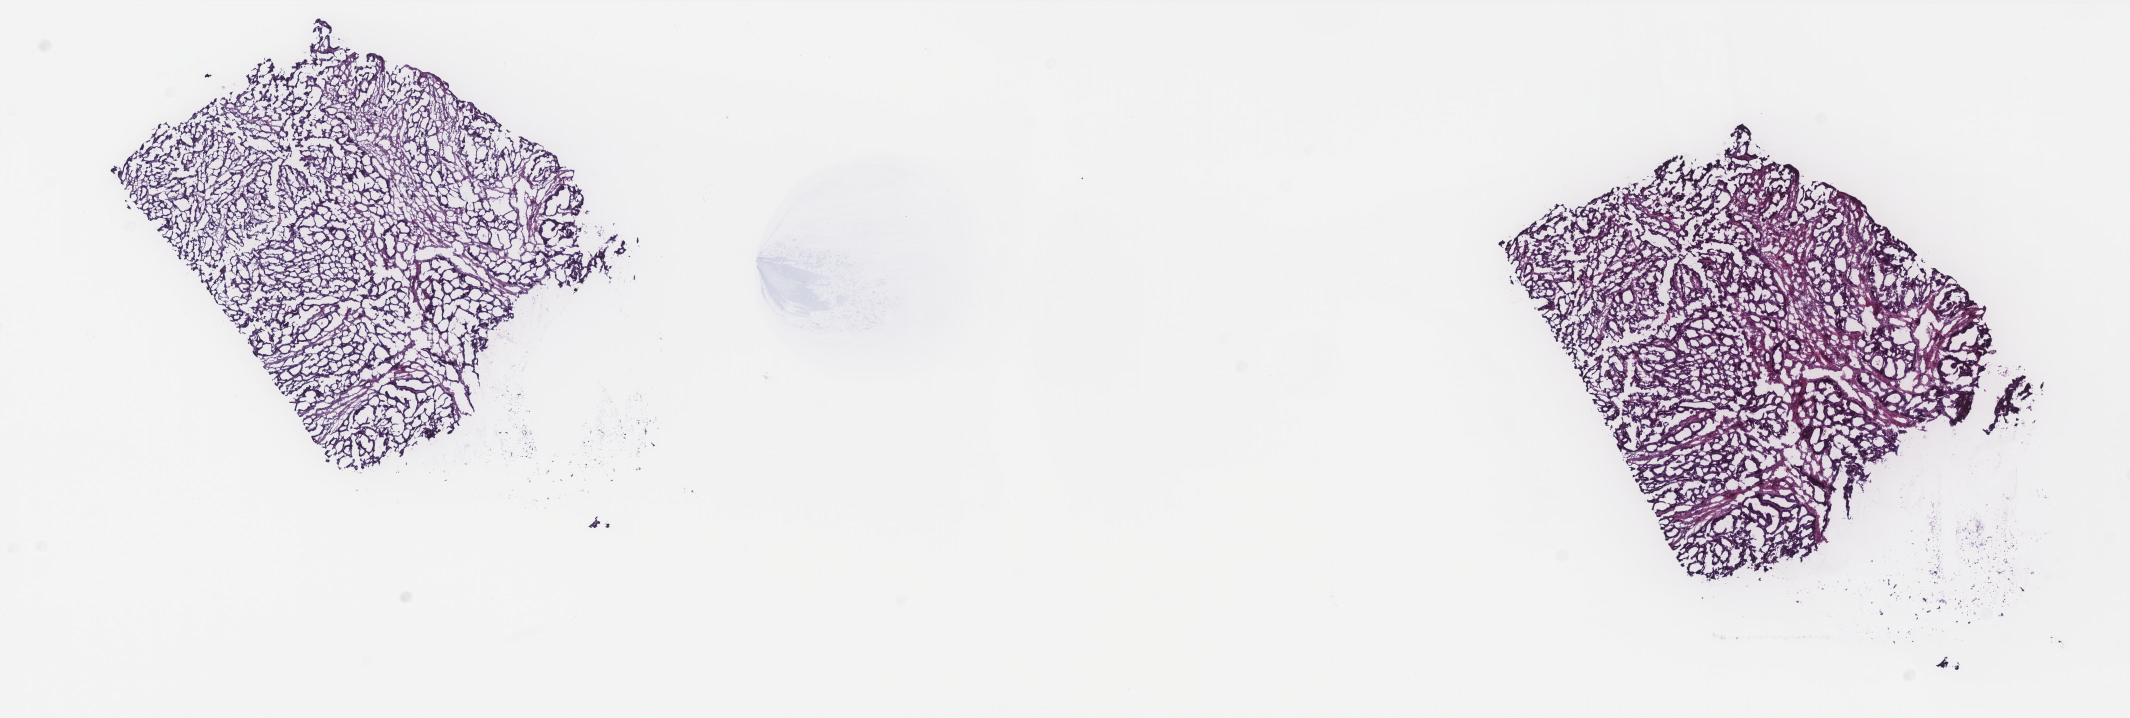
Whole-slide histology image, H&E-stained — a low-resolution overview of the entire scanned area, about 17.1 x 5.8 mm; frozen section from the top of the tissue portion; sample: primary tumour, rectum. Patient: female, age at initial diagnosis 77 years. Composition of this section per pathologist review: tumour cells 100%, tumour nuclei 80%, normal cells 0%, stromal cells 0%, necrosis 0%. Infiltration values recorded for this section: lymphocyte infiltration 0%, monocyte infiltration 0%, neutrophil infiltration 0%.
Diagnosis: Adenocarcinoma, NOS. TNM: T2 N1 M0. Lymph nodes positive (case pathology): 1 of 7 examined. AJCC pathologic stage: IIIA.